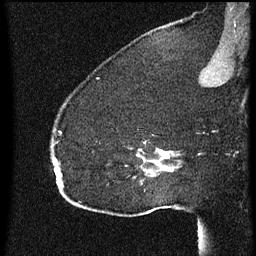
Breast MRI (dynamic contrast-enhanced), one sagittal slice; dynamic contrast-enhanced series, image 2 of 3 at this slice position (ordered by acquisition); 1.5 T; TE 4.2 ms, TR 8 ms; 256 × 256 image matrix. Female patient, age 52 years.
Outlined on this slice (semi-automatic segmentation, software-assisted and operator-edited):
- analysis volume of interest (the breast-tissue region the enhancement analysis was run in; not a lesion): bounding box <54,122,178,207> (left, top, right, bottom; pixels)
- tumour enhancement mask (voxels above the 70 % enhancement threshold inside the analysis volume of interest): <55,142,170,177>